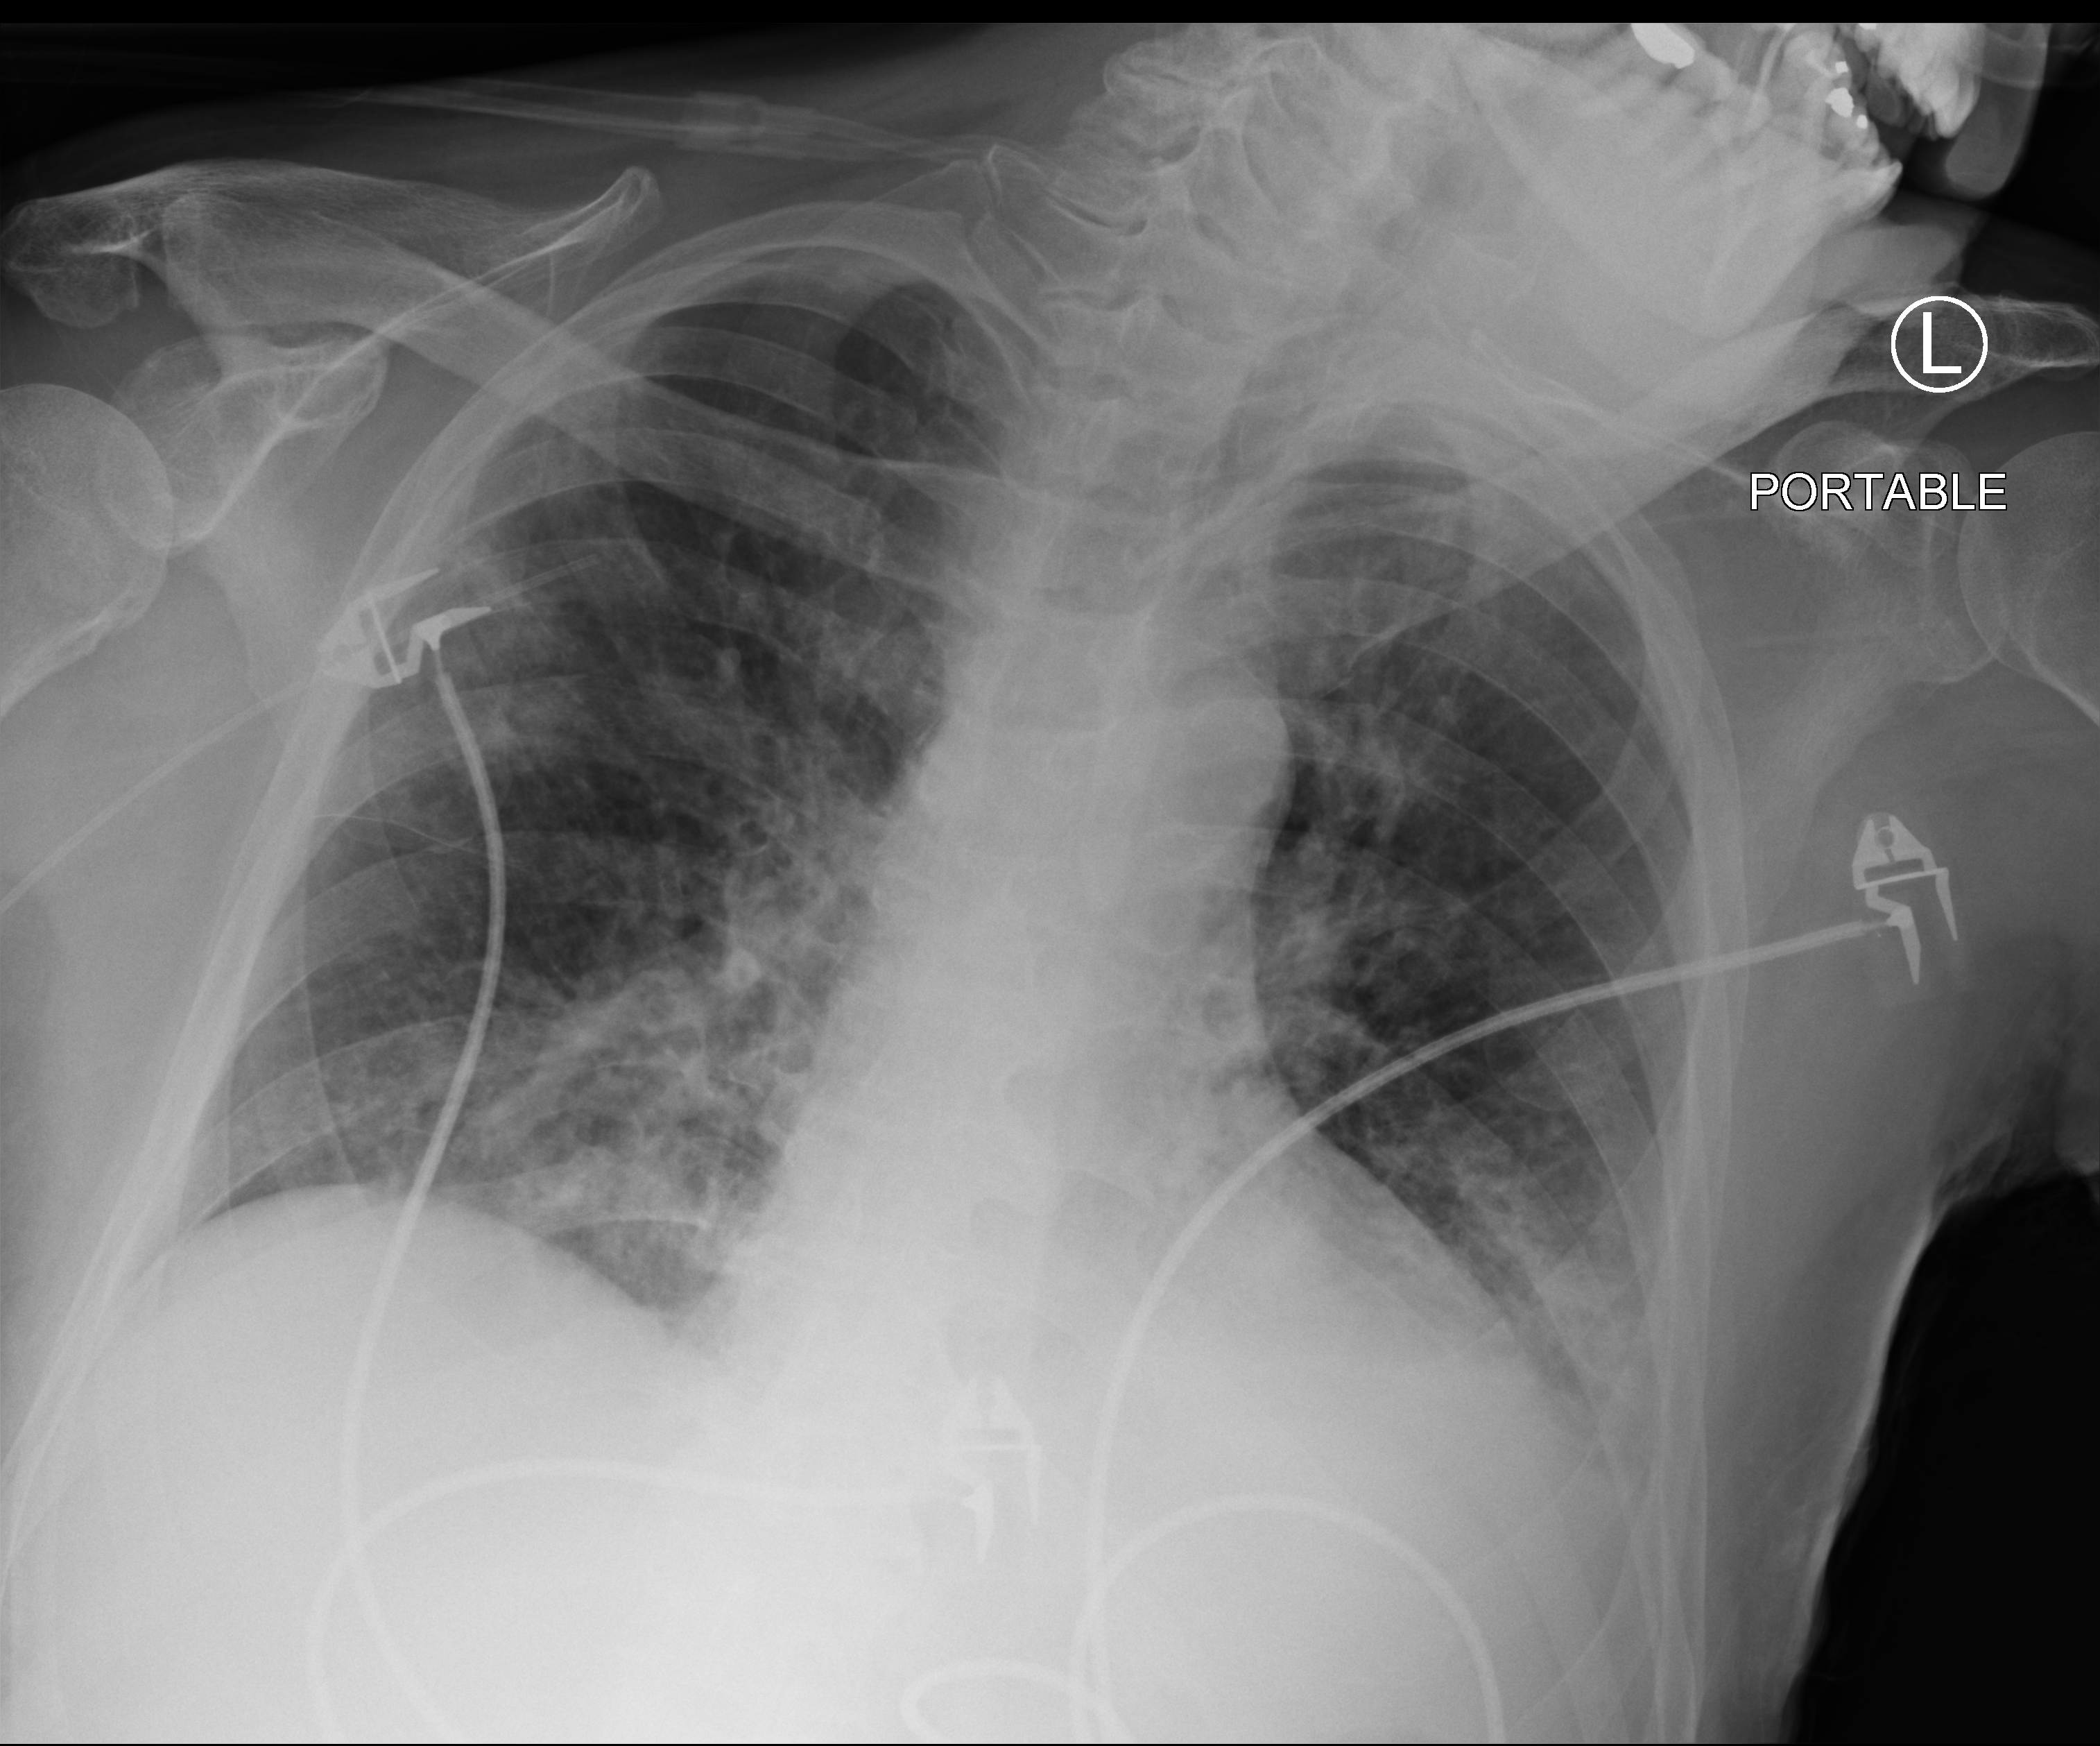
Bedside chest radiograph (computed radiography), anteroposterior (AP) projection. Male patient hospitalised with COVID-19, age 60–74 years.
Admission-level facts for this patient (not findings on this image; timing relative to this image not recorded): hypertension (admission record): yes; chronic kidney disease (admission record): no.